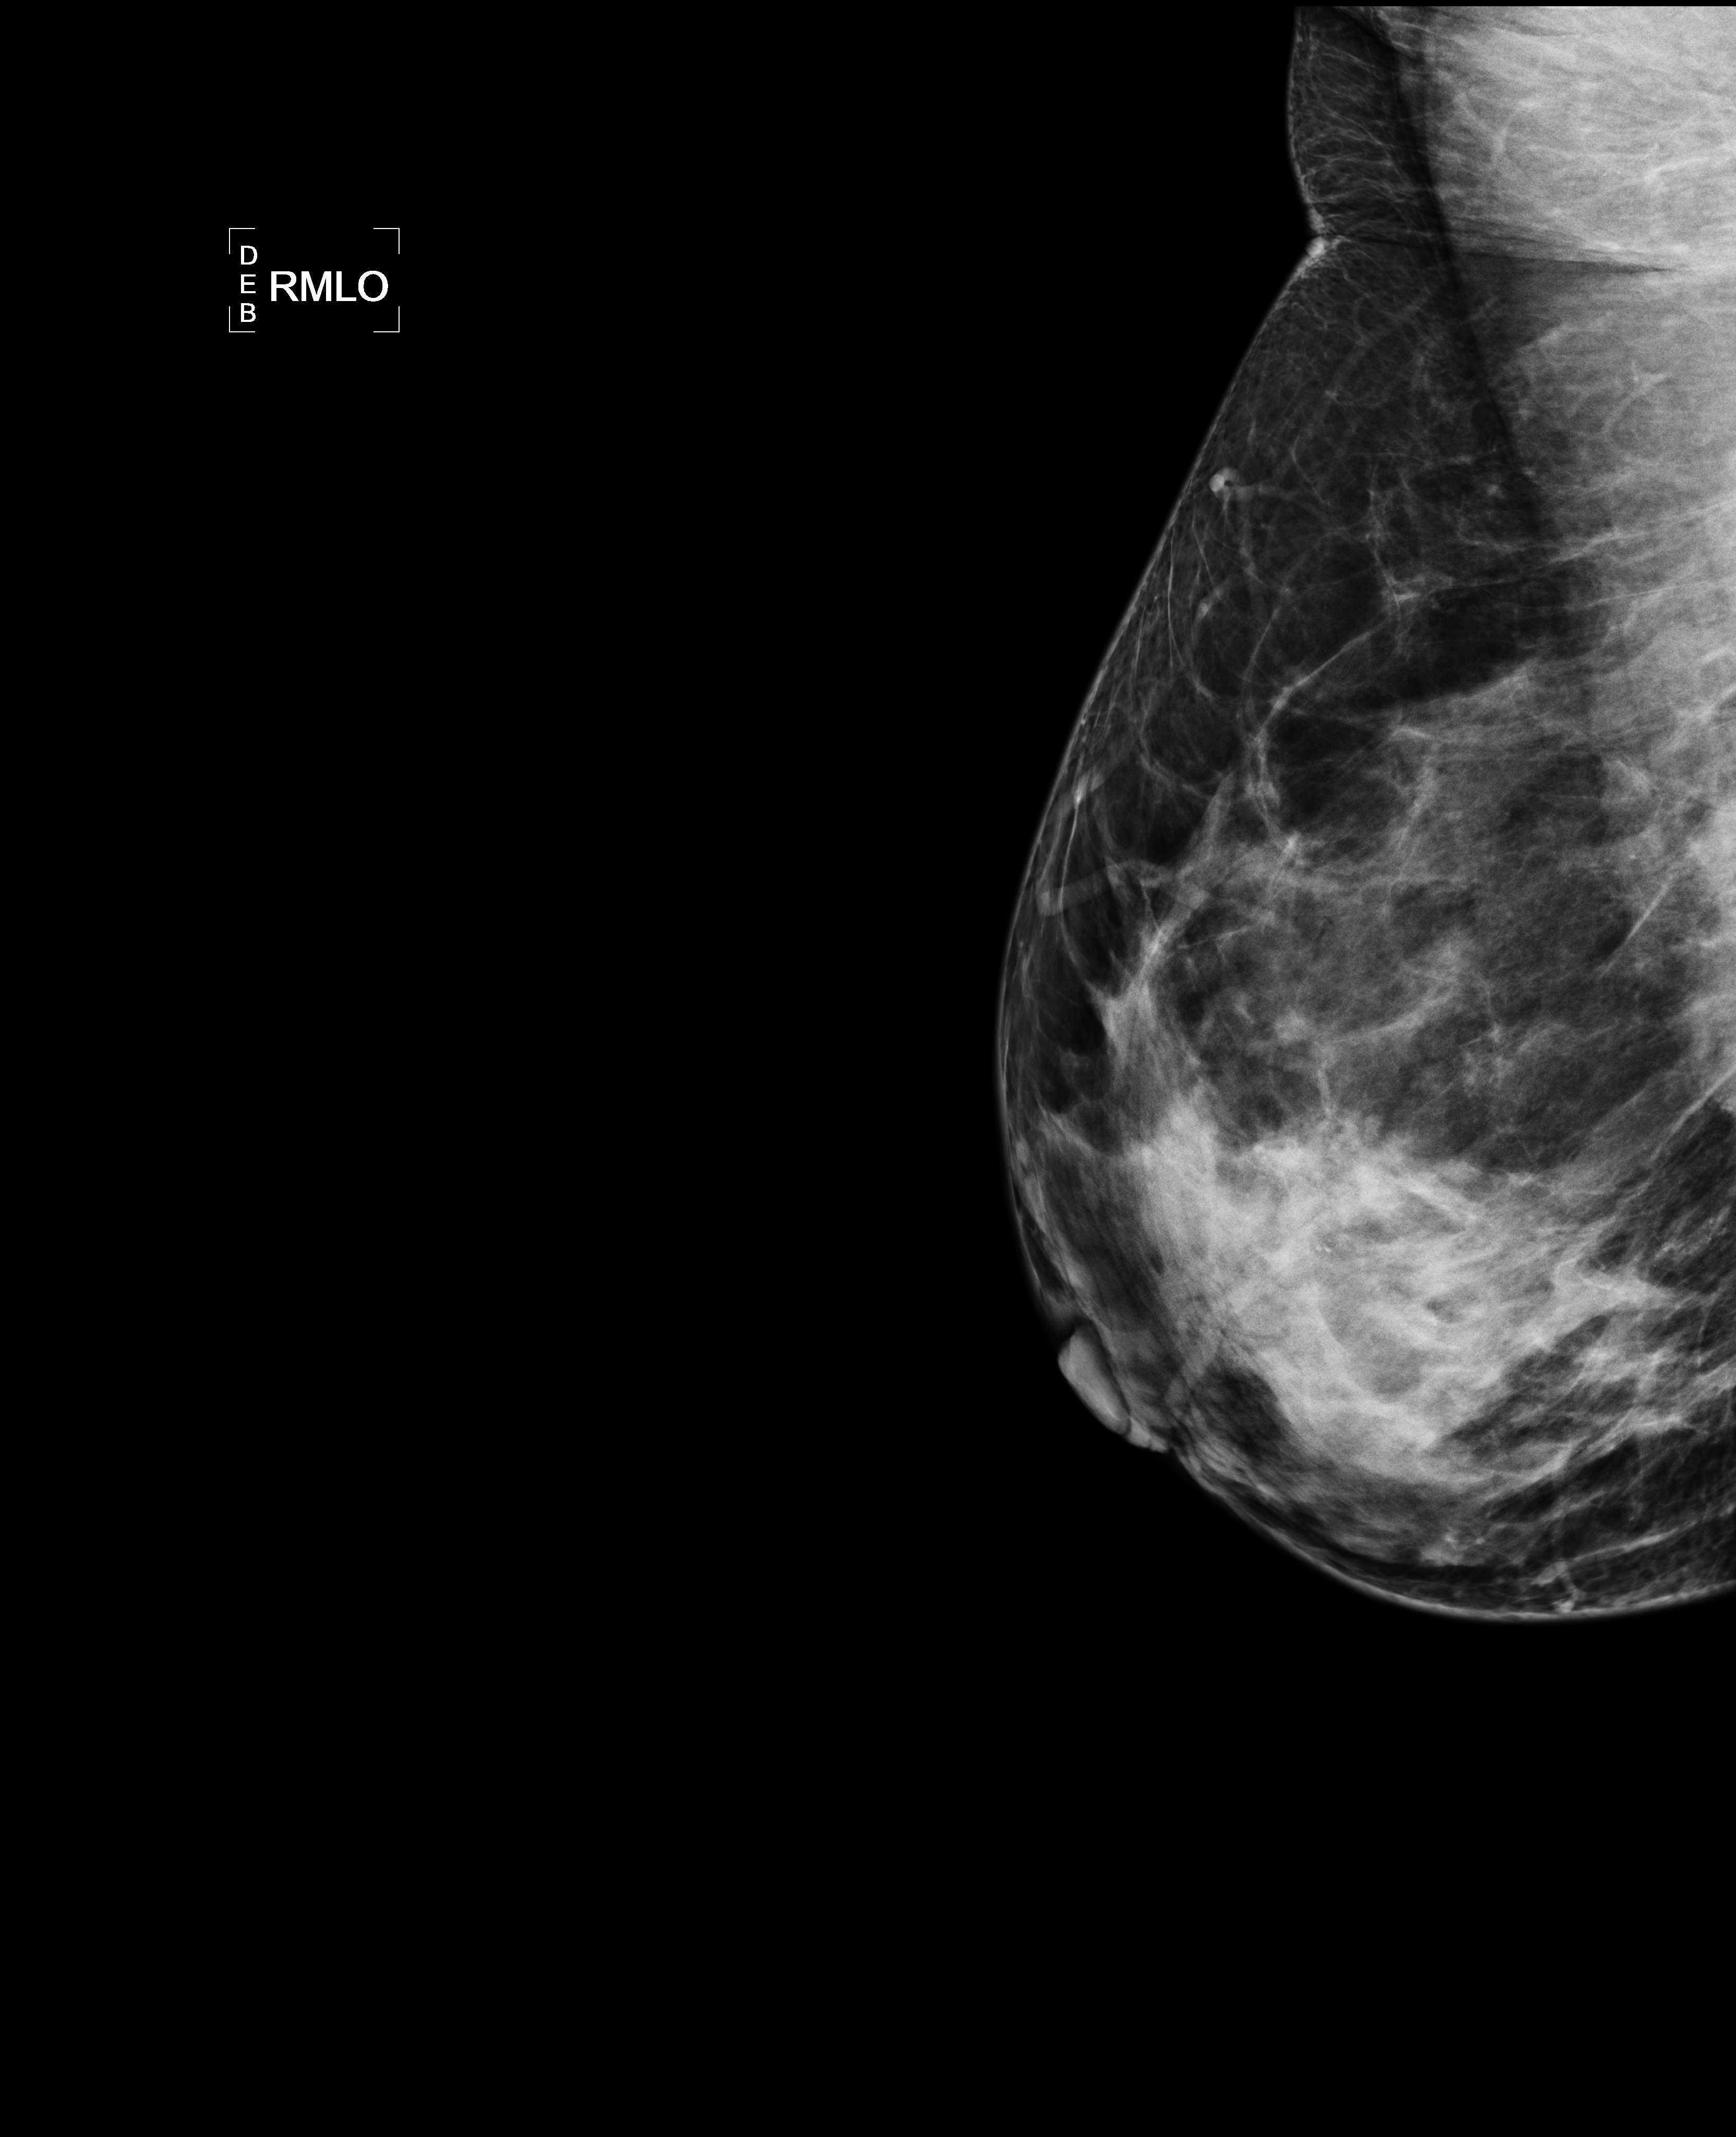
Mammogram, right breast, MLO view.
Patient-level pathology facts (clinical record, not image findings): pathology diagnosis: INVASIVE DUCTAL CARCINOMA, MODIFIED SCARFF-BLOOM-RICHARDSON GRADE-I/III. A LESS THAN 5% INTRADUCTAL CARCINOMA COMPONENT, NUCLEAR GRADE-II/III, IS ALSO PRESENT. (left breast); receptor status (as recorded): ER pos (strong), PR pos (strong), HER2 pos; pathology report notes: mastectomy; INVASIVE DUCTAL CARCINOMA, MODIFIED SCARFF-BLOOM-RICHARDSON GRADE-I/III. A LESS THAN 5% INTRADUCTAL CARCINOMA COMPONENT, NUCLEAR GRADE-II/III, IS ALSO PRESENT; clinical background (as recorded): early 40s with left breast cancer. LMP unknown.